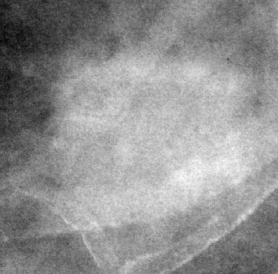
Crop from a digitized film mammogram around one marked abnormality; right breast; MLO view; BI-RADS breast density category 3 (scale 1–4).
Finding: mass, shape irregular, margins obscured / ill defined; BI-RADS assessment category 4; subtlety rating 3 on a 1 (subtle) to 5 (obvious) scale; pathology result (as recorded, not read from the image): malignant.